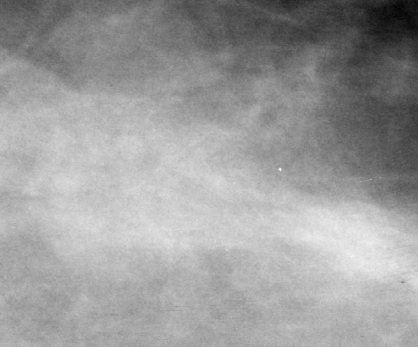
Cropped region of a digitized screen-film mammogram centred on a radiologist-marked abnormality; left breast; CC view.
Marked abnormality: mass, shape irregular, margins ill defined; BI-RADS assessment category 3; subtlety rating 3 on a 1 (subtle) to 5 (obvious) scale; pathology result (as recorded, not read from the image): benign.